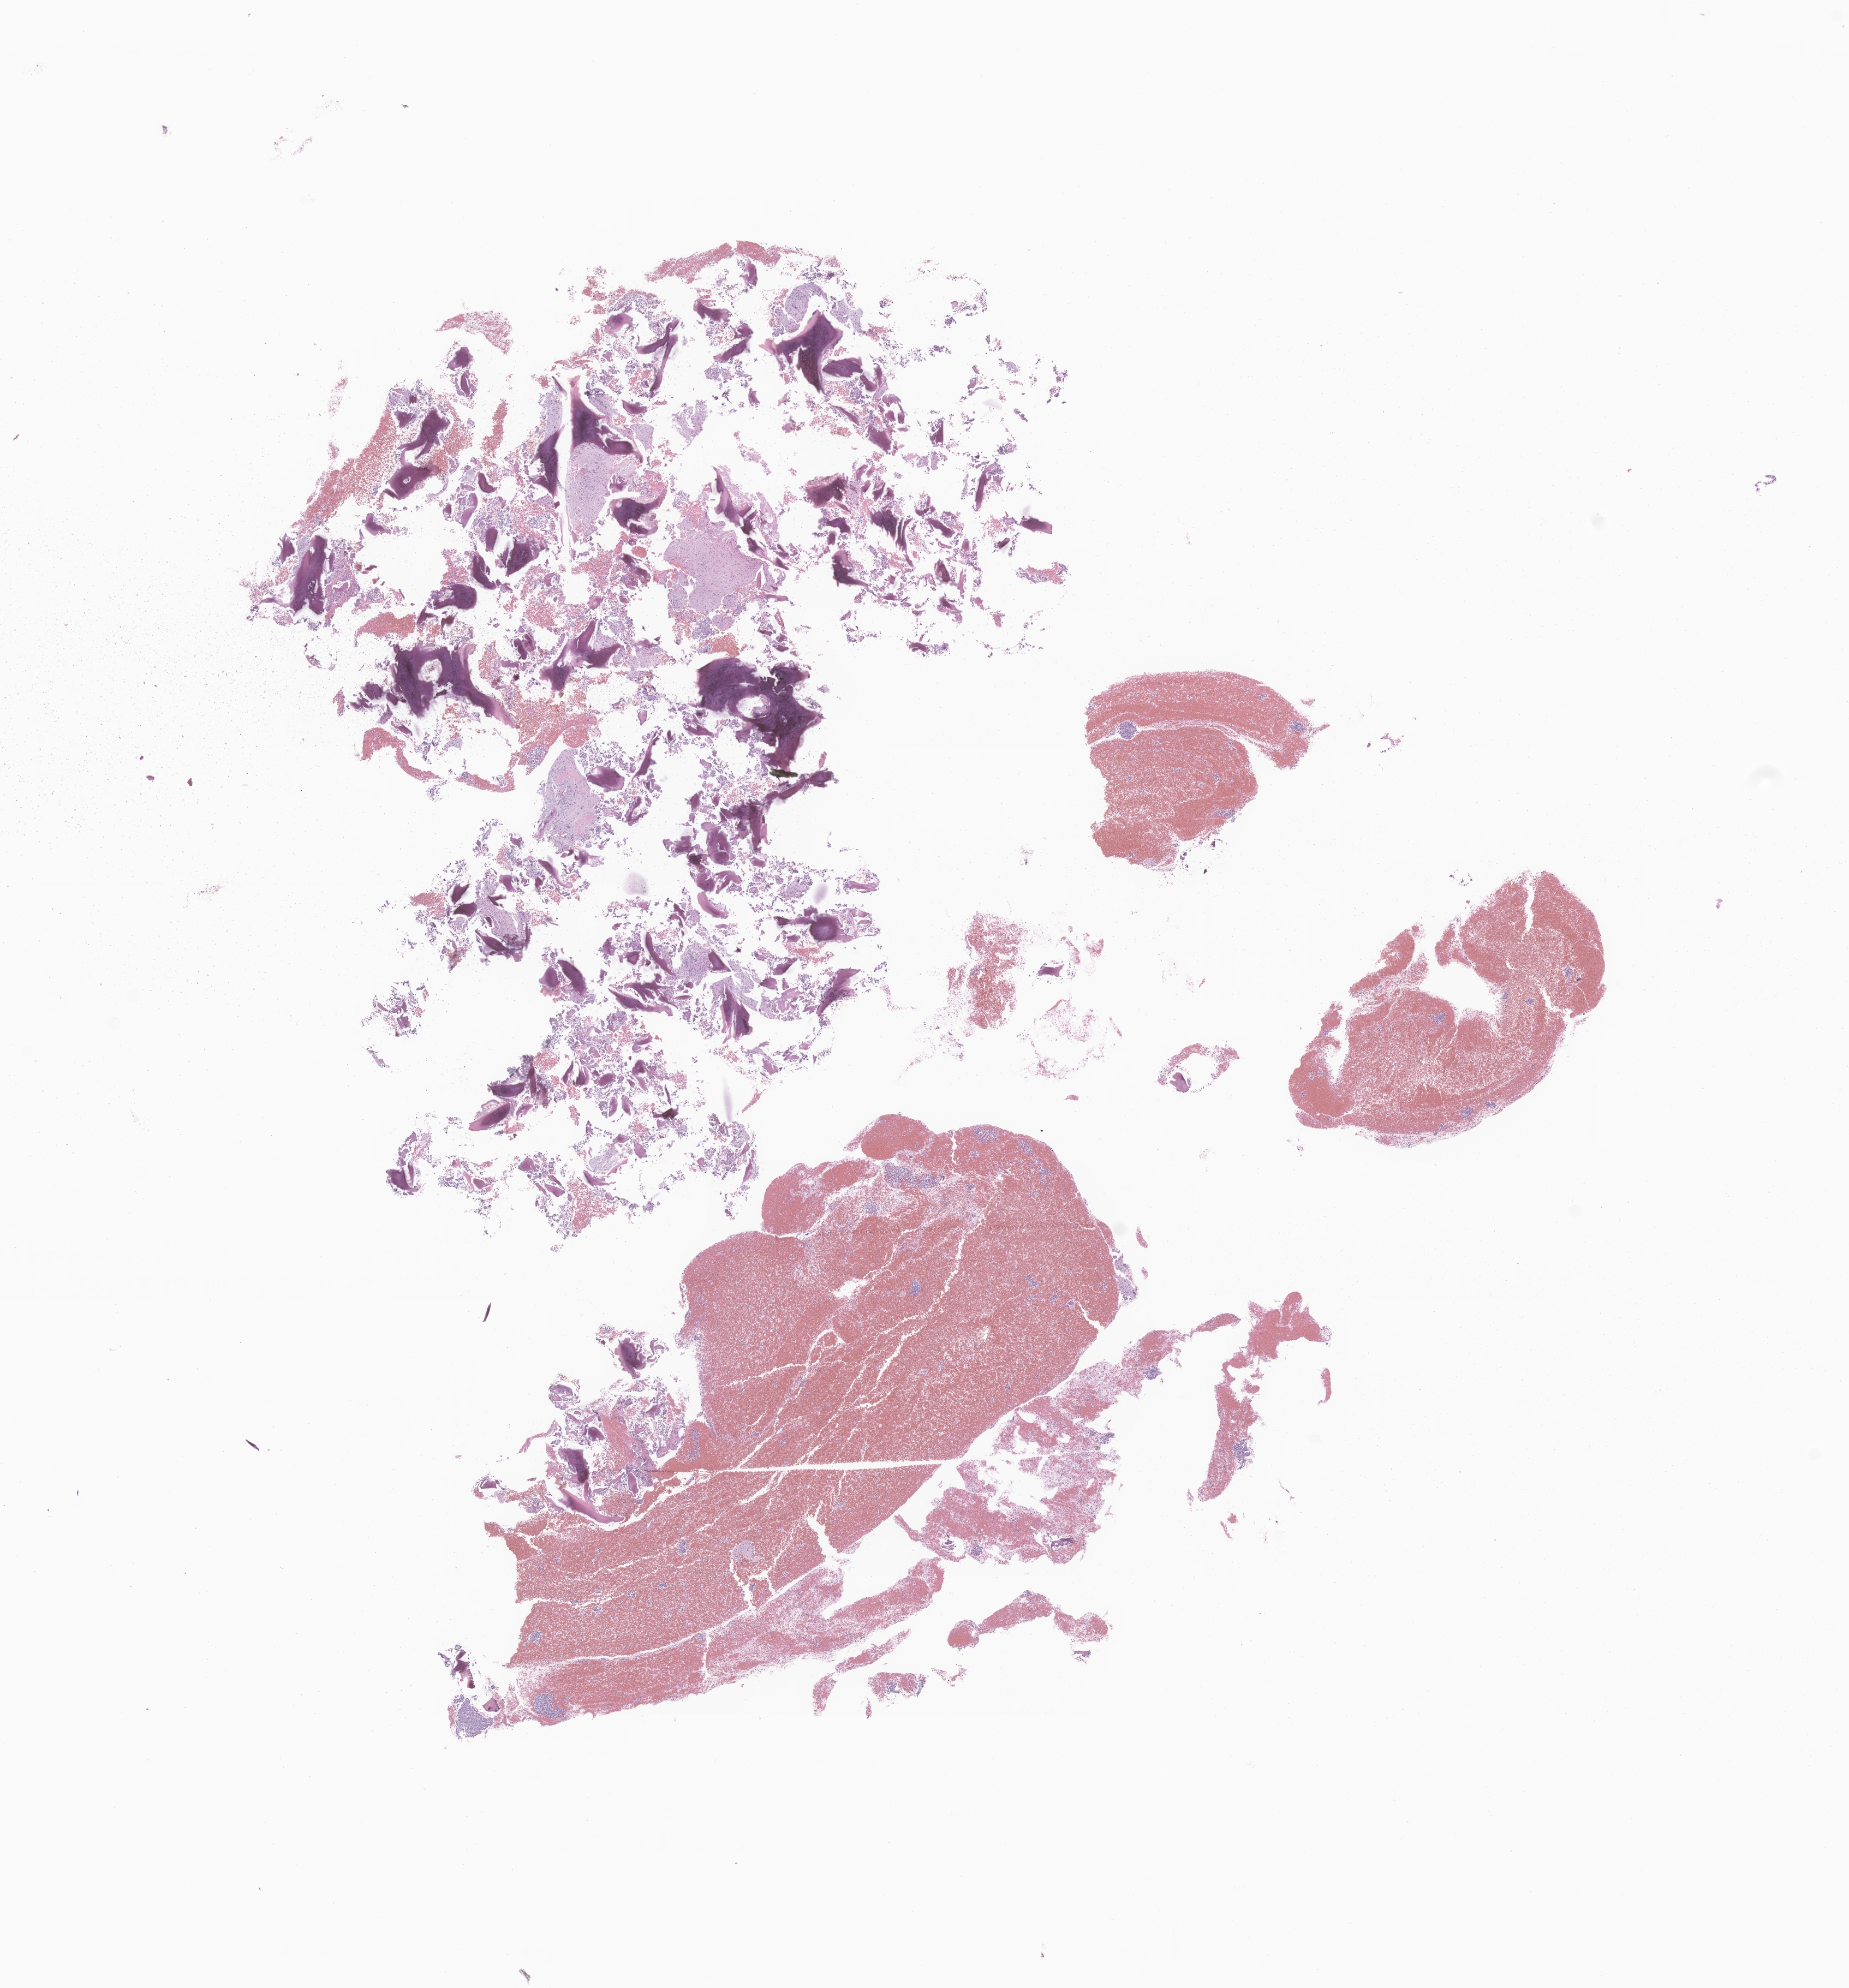
Hematoxylin and eosin (H&E) whole-slide image of tumor tissue from the pelvis, a low-resolution overview of the entire scanned area, about 14.3 x 15.4 mm. FFPE section. Patient female; age 195 months (16 years 3 months).
Recorded diagnosis: Clear cell sarcoma, NOS.